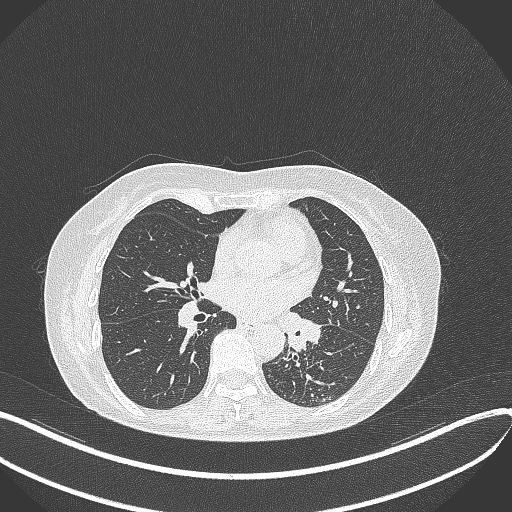
Chest CT, one axial slice. Position 202 of 429 along the scan axis. Reconstruction kernel B70f. Lung window (W 1500 / L -600 HU). 1 mm slice thickness. 512 × 512 image matrix, field of view 400 × 400 mm. Patient: female, 63 years. From the clinical record (not read from this slice): clinical TNM (as recorded): T1b N0 M0.
Structures marked on this image (rectangle marked by the reading radiologist):
- lung tumour (recorded histology: adenocarcinoma): box from (x=284, y=308) to (x=330, y=357) px